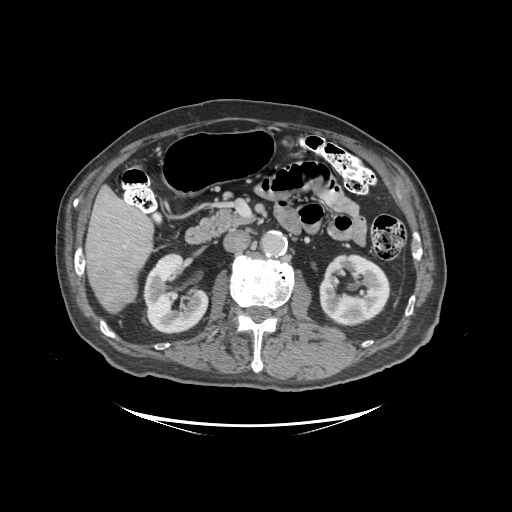
Contrast-enhanced abdominal CT (liver protocol), one axial slice. Slice 41 of 99 in the series (ordered by position). Reconstruction kernel STANDARD. Soft-tissue window (W 400 / L 40 HU). 2.5 mm slice thickness. 512 × 512 image matrix, field of view 460 × 460 mm. Case-level facts recorded for this patient, not image findings: diagnosis: hepatocellular carcinoma (patient treated with transarterial chemoembolisation; whether this scan precedes or follows treatment is not stated here); TNM stage (as recorded): Stage-I; Child-Pugh class: A.
Structures marked on this image (semi-automatically segmented with operator editing):
- liver parenchyma outside the tumour (the mass and vessels are separate outlines, so this box may not span the whole liver): bounding box (x1, y1, x2, y2) in pixels: (86, 186, 154, 312)
- mass: (87, 255, 135, 310)
- liver vessels: (141, 209, 144, 211)